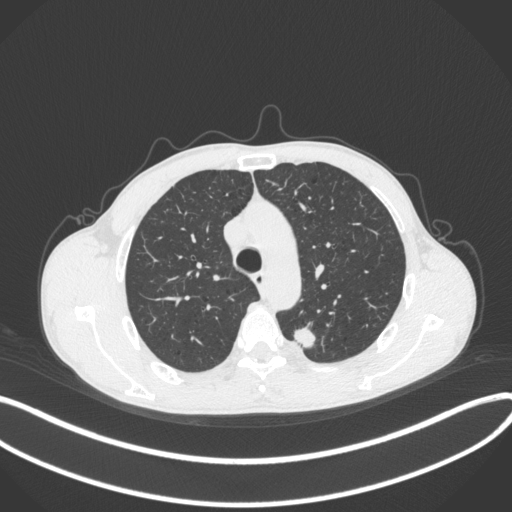
Chest CT, one axial slice. Slice 292 of 429 in the series (ordered by position). Reconstruction kernel B31f. 120 kVp. Lung window (W 1500 / L -600 HU). 1 mm slice thickness. 512 × 512 image matrix. Patient: male, 51 years. From the clinical record (not read from this slice): clinical TNM (as recorded): T2a N1 M1.
Structures marked on this image (rectangle marked by the reading radiologist):
- lung tumour (recorded histology: adenocarcinoma): bounding box <293,325,319,350> (left, top, right, bottom; pixels)